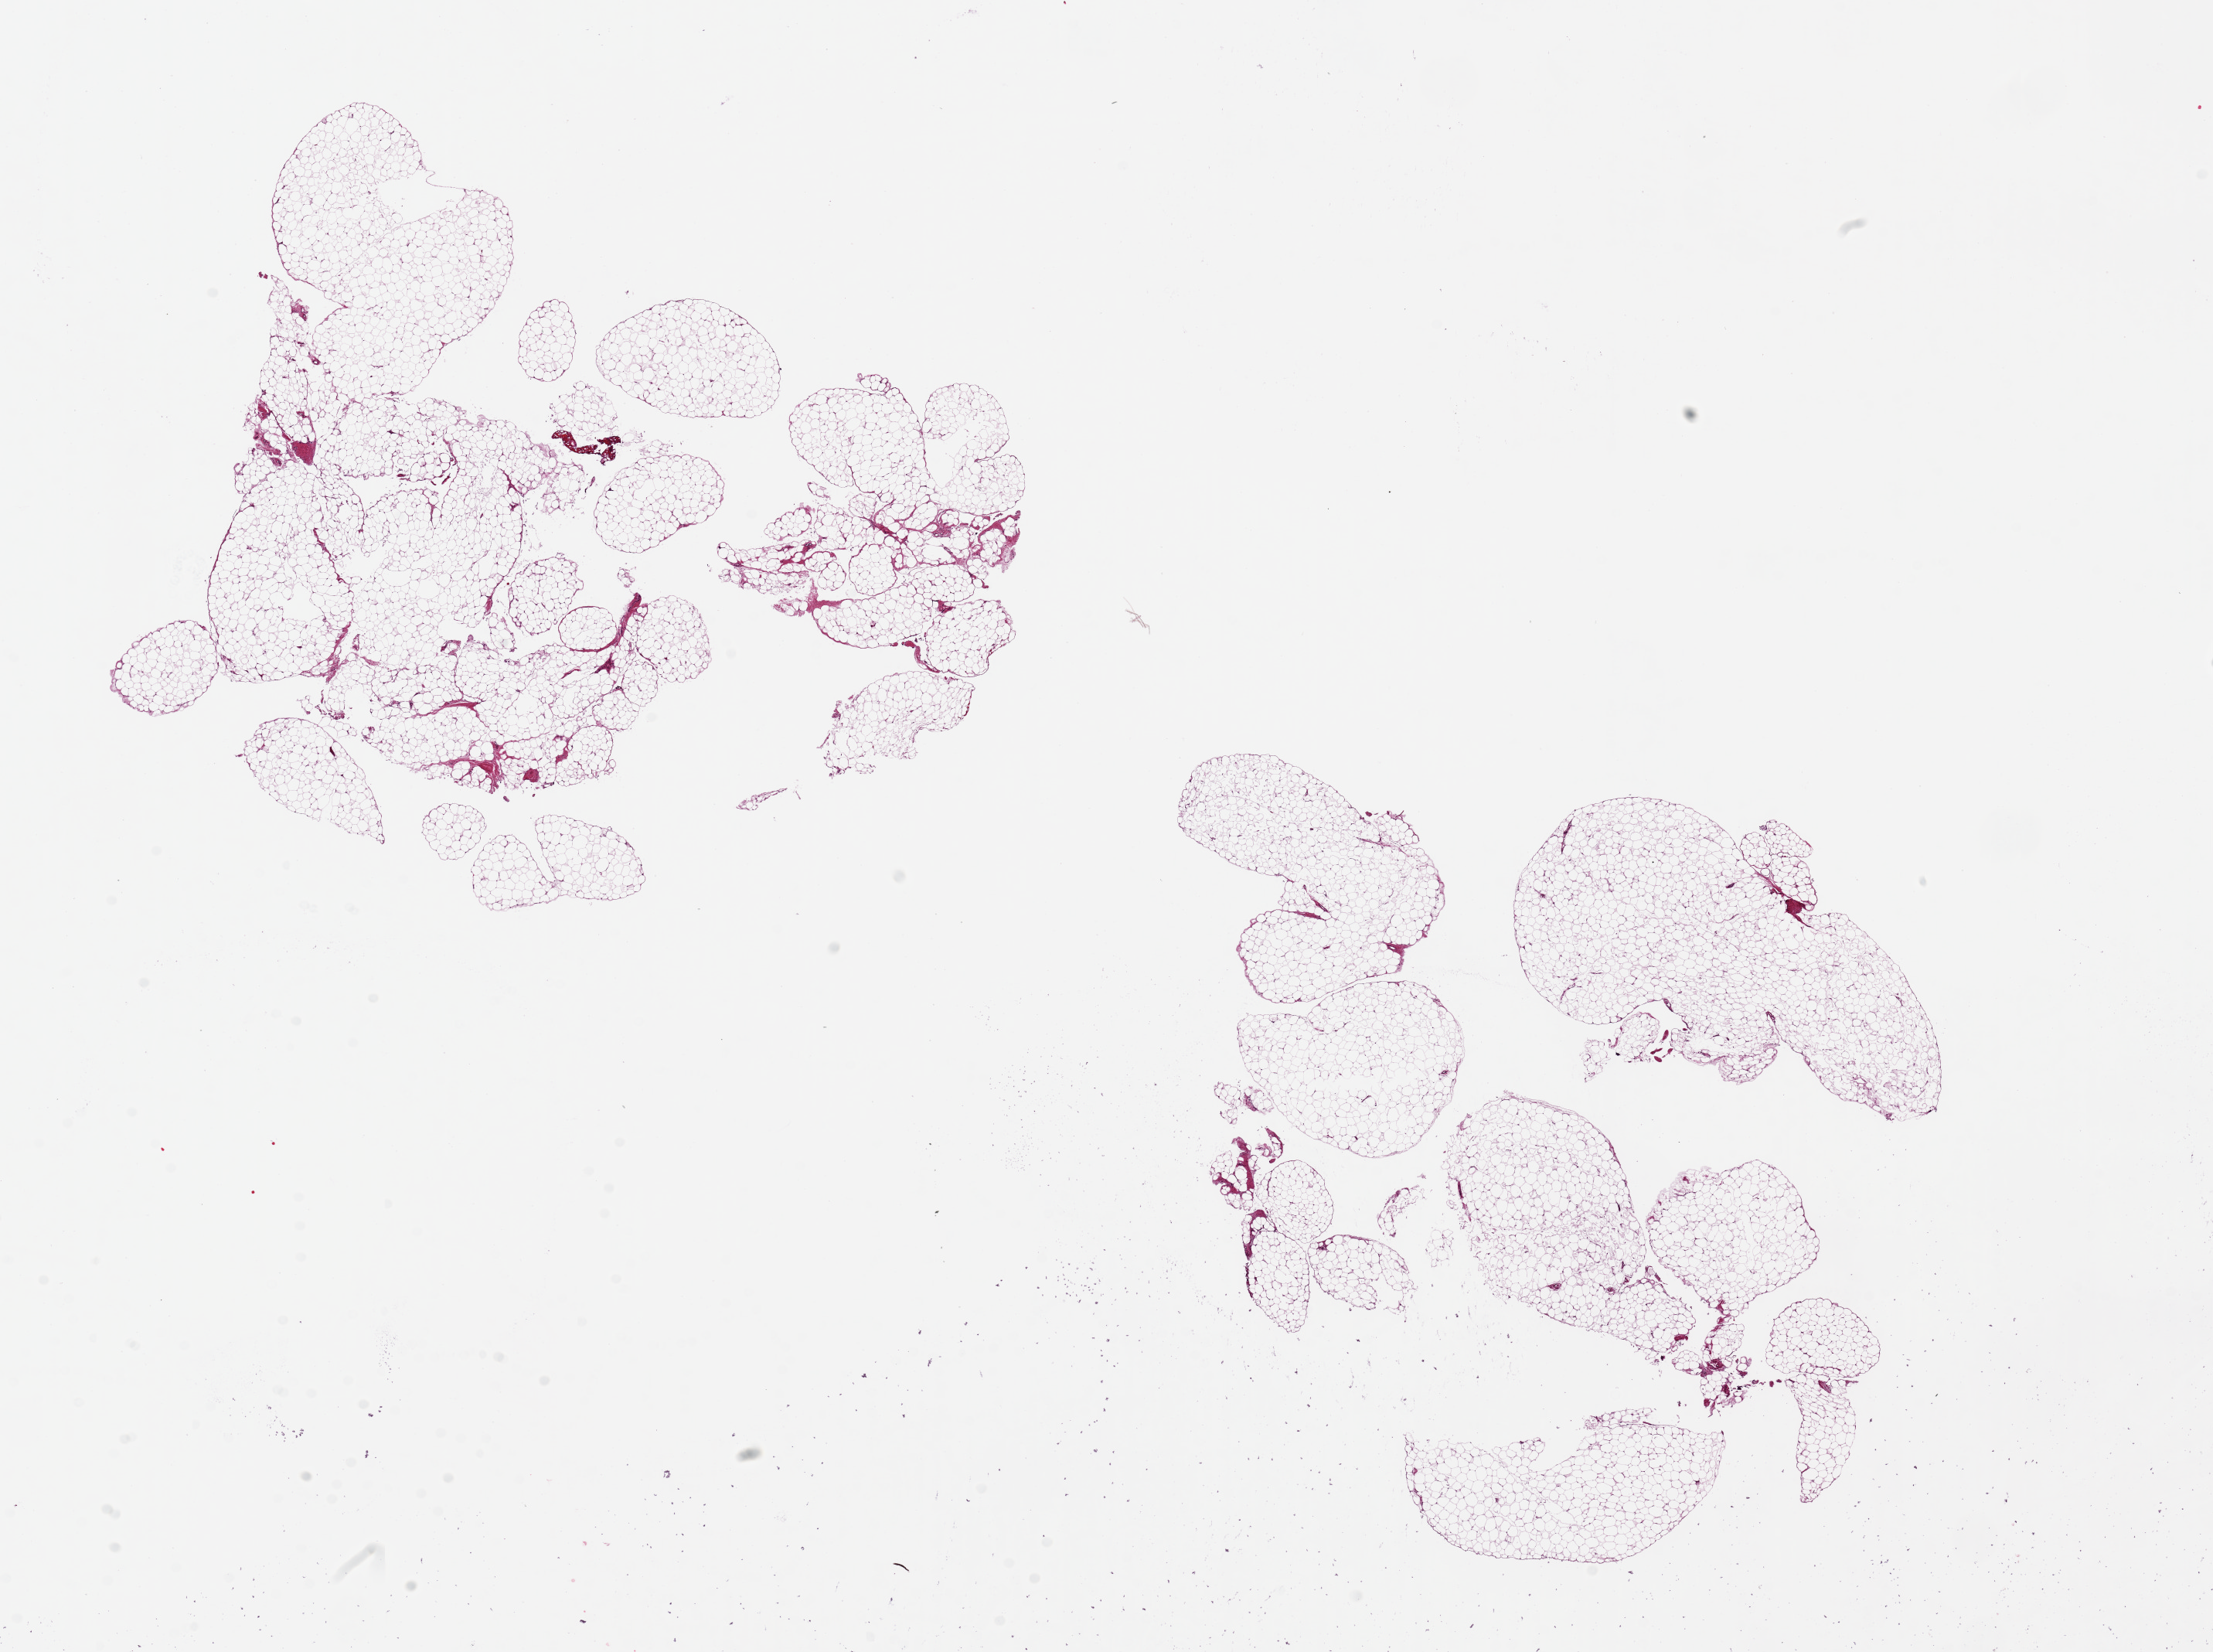
H&E whole-slide image, brightfield, a low-resolution overview of the entire scanned area, about 22.6 x 16.9 mm; PAXgene-fixed paraffin-embedded (PFPE) section; section of omentum (target tissue); tissue donor sample. Donor: male.
Pathologist's review note for this sample: 2 pieces, 9x7 & 10x7mm; lobulated, no fixation artifacts.